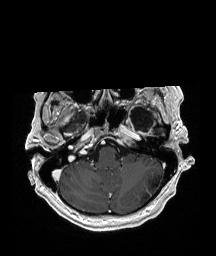
Brain MRI from a brain-tumour surgery series, one axial slice; position 149 of 192 along the scan axis; T1-weighted post-contrast; 216 × 256 image matrix, field of view 211 × 250 mm. Case-level facts recorded for this patient, not image findings: histopathology: Glioblastoma; WHO grade: 4; IDH mutation: no.
Annotated regions visible in this slice (expert manual segmentation):
- previous resection cavity: bounding box <128,107,155,132> (left, top, right, bottom; pixels)